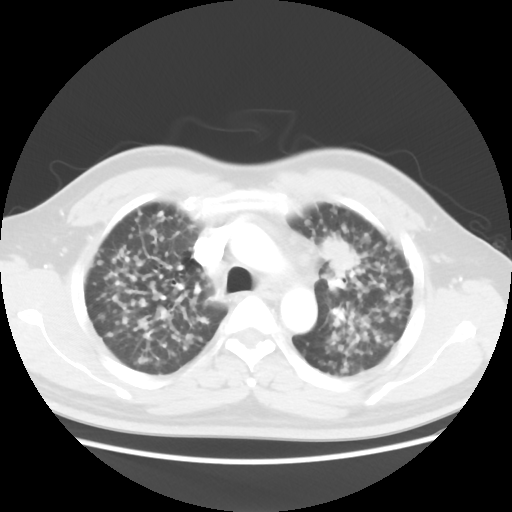
Chest CT, one axial slice. Slice 28 of 40 in the series (ordered by position). Lung window (W 1500 / L -600 HU). 5 mm slice thickness. 512 × 512 image matrix, field of view 366 × 366 mm. Male patient, age 41 years. From the clinical record (not read from this slice): clinical TNM (as recorded): T1c N3 M1b; histopathological grade: G2-3.
Structures marked on this image (rectangle marked by the reading radiologist):
- lung tumour (recorded histology: adenocarcinoma): bounding box <316,236,364,283> (left, top, right, bottom; pixels)